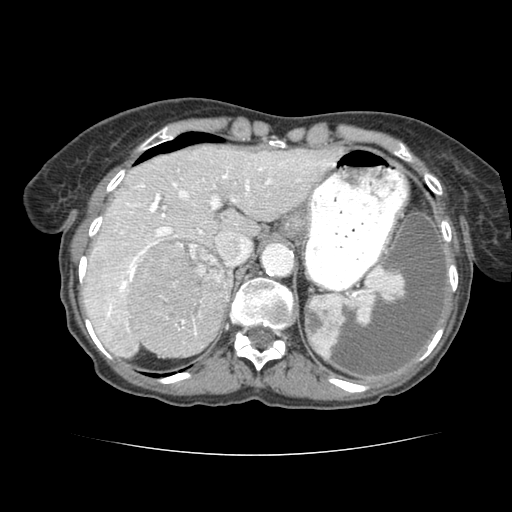
Contrast-enhanced abdominal CT (liver protocol), one axial slice; slice 57 of 77 in the series (ordered by position); soft-tissue window (W 400 / L 40 HU); 512 × 512 image matrix, field of view 340 × 340 mm. From the clinical record (not read from this slice): diagnosis: hepatocellular carcinoma (patient treated with transarterial chemoembolisation; whether this scan precedes or follows treatment is not stated here); TNM stage (as recorded): Stage-I; Child-Pugh class: A; tumour differentiation: well differentiated; tumour nodularity: uninodular.
Annotated regions visible in this slice (semi-automatic segmentation, software-assisted and operator-edited):
- liver parenchyma outside the tumour (the mass and vessels are separate outlines, so this box may not span the whole liver): bounding box [x1, y1, x2, y2] px = [80, 144, 330, 354]
- mass: [125, 238, 228, 352]
- liver vessels: [97, 167, 240, 293]